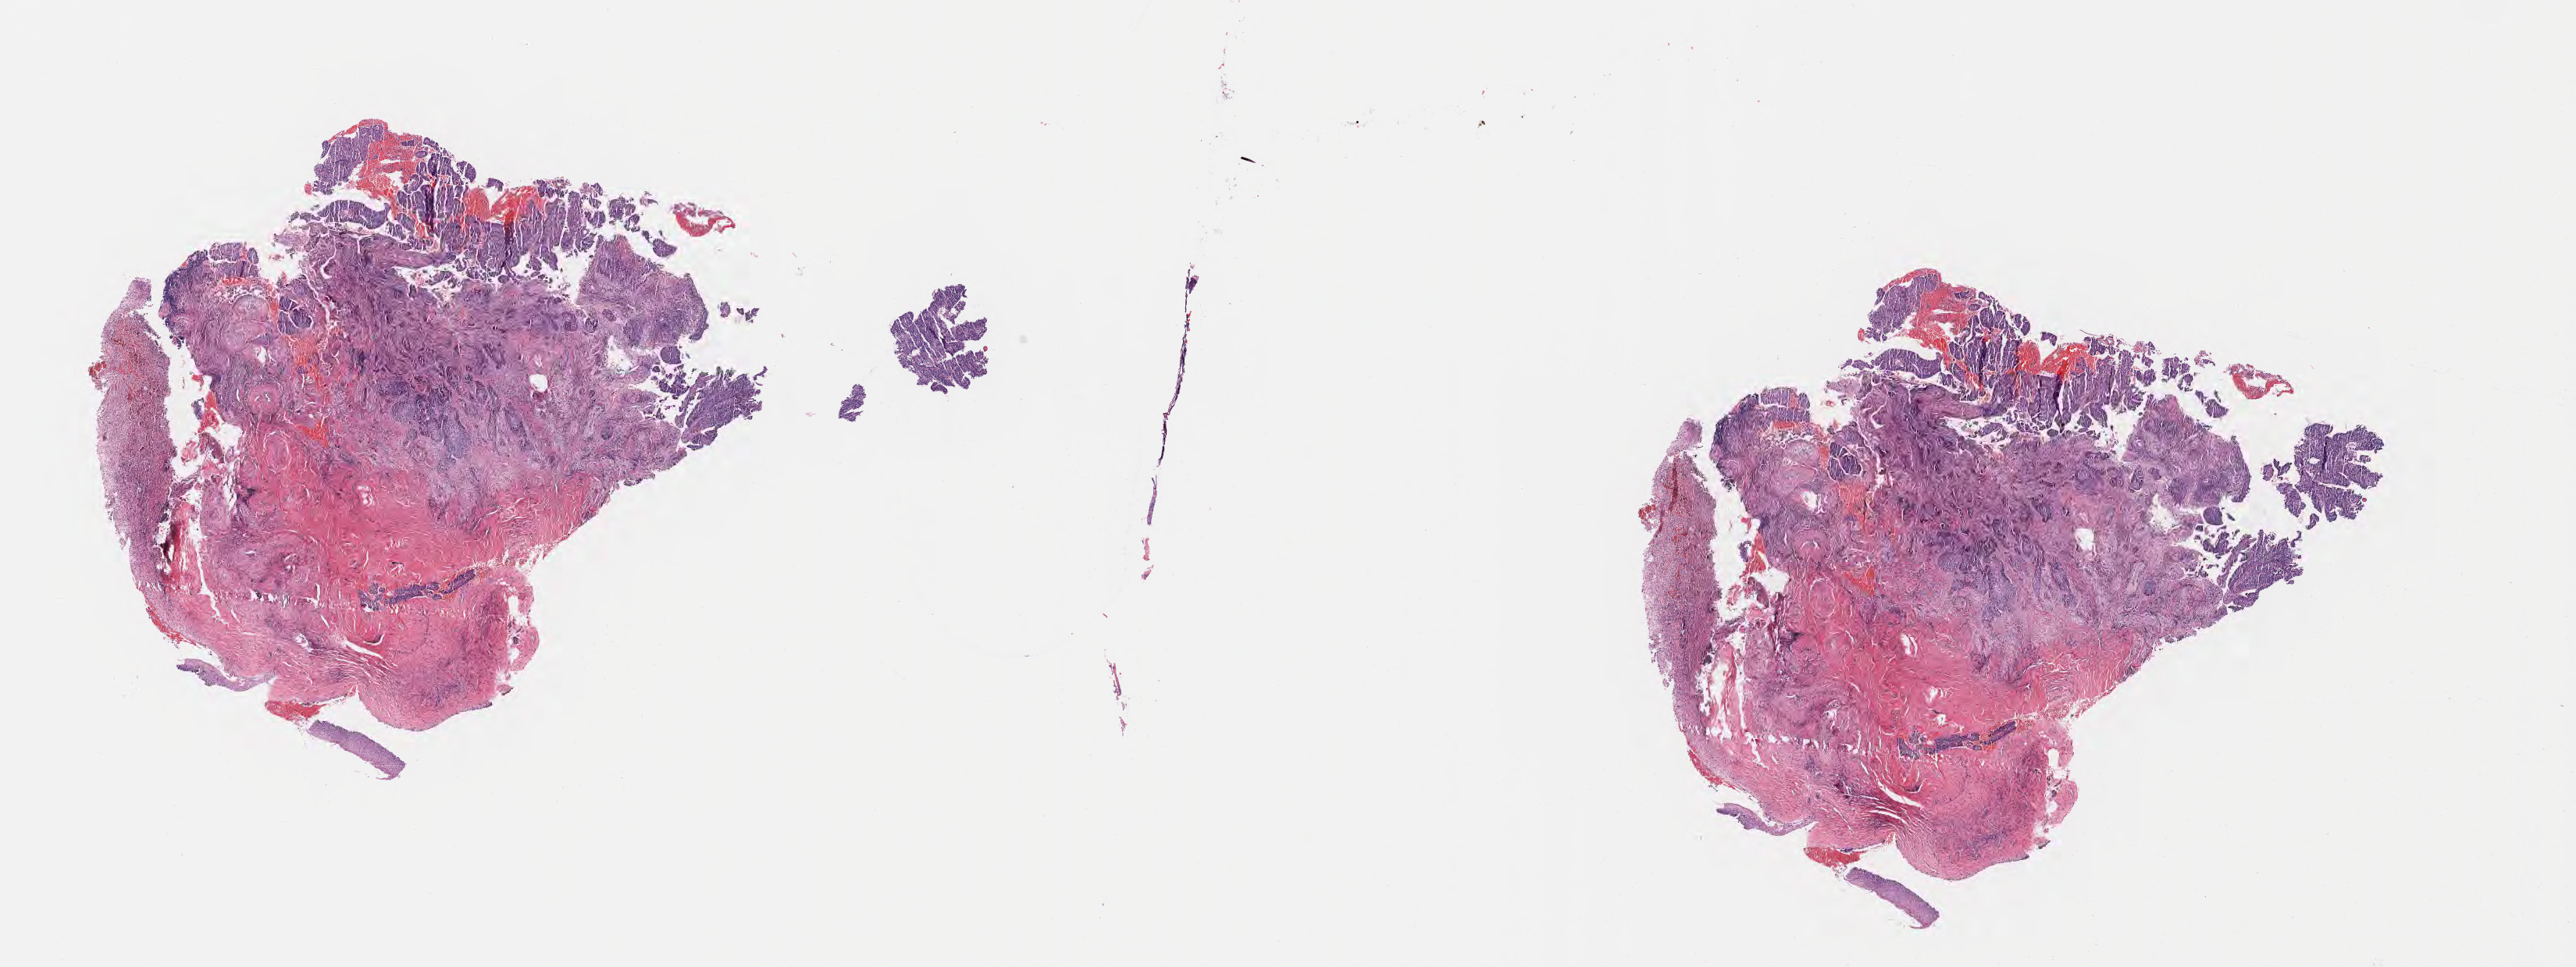
Hematoxylin and eosin (H&E) whole-slide image, shown as a low-resolution overview of the whole scanned area (about 26.7 x 10.0 mm). Specimen: tumor tissue. Anatomic site: cervix. Patient female; aged 45.
Histologic diagnosis: Squamous cell carcinoma, large cell, nonkeratinizing, NOS.